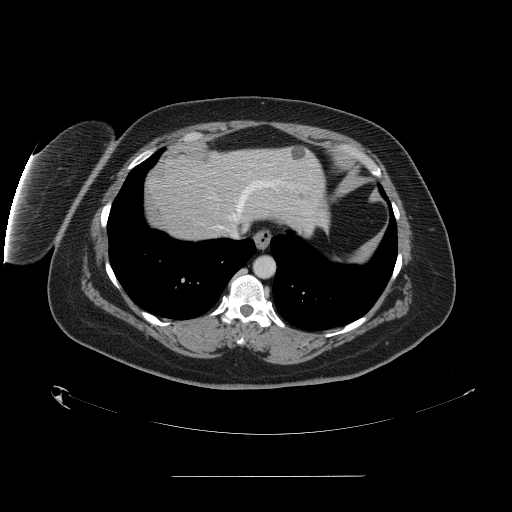
Contrast-enhanced abdominal CT, one axial slice; position 135 of 164 along the scan axis; 120 kVp; intravenous contrast given; soft-tissue window (W 400 / L 40 HU); 512 × 512 image matrix, field of view 495 × 495 mm. Female patient, age 52 years. From the clinical record (not read from this slice): diagnosis: colorectal cancer liver metastases, imaged before liver resection; multiple liver metastases: yes; largest metastasis: 3.5 cm; disease in both lobes: no.
Structures marked on this image (manually delineated by an expert):
- hepatic veins: box from (x=219, y=181) to (x=278, y=238) px
- liver: (x=148, y=147)–(x=327, y=241)
- planned liver remnant (the part of the liver to remain after resection): (x=174, y=147)–(x=328, y=227)
- liver metastasis: (x=290, y=149)–(x=306, y=160)